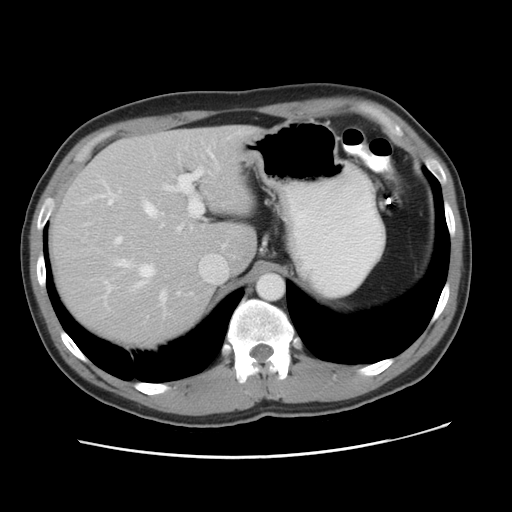
Contrast-enhanced abdominal CT, one axial slice. Slice 35 of 49 in the series (ordered by position). Reconstruction kernel STANDARD. Intravenous contrast given. Soft-tissue window (W 400 / L 40 HU). 5 mm slice thickness. 512 × 512 image matrix, field of view 363 × 363 mm. Male patient, age 41 years. From the clinical record (not read from this slice): diagnosis: colorectal cancer liver metastases, imaged before liver resection; multiple liver metastases: yes; largest metastasis: 0.7 cm; disease in both lobes: yes.
Annotated regions visible in this slice (outlined manually by an expert reader):
- hepatic veins: bounding box (x1, y1, x2, y2) in pixels: (92, 157, 228, 304)
- liver: (50, 126, 256, 348)
- planned liver remnant (the part of the liver to remain after resection): (100, 126, 256, 271)
- portal vein (with intrahepatic branches): (105, 150, 212, 294)